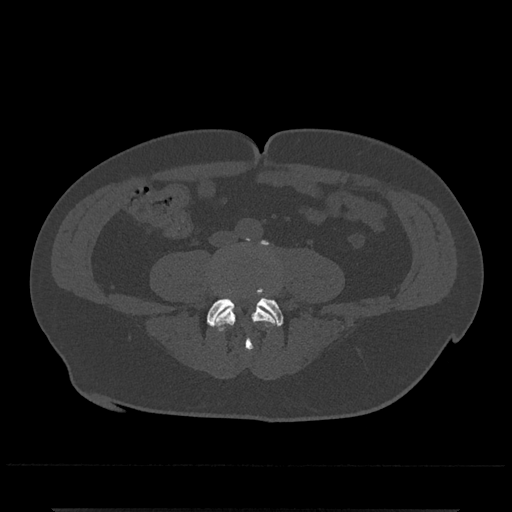
CT including the spine, one axial slice; position 121 of 797 along the scan axis; reconstruction kernel Br40s/3; 120 kVp; bone window (W 1800 / L 400 HU); 0.5 mm slice thickness; 512 × 512 image matrix, field of view 393 × 393 mm. Male patient, age 67 years. From the clinical record (not read from this slice): primary cancer: prostate.
Structures marked on this image (semi-automatically segmented with operator editing):
- L4 vertebra: bounding box (x1, y1, x2, y2) in pixels: (212, 240, 279, 352)
- L5 vertebra: (207, 291, 283, 326)